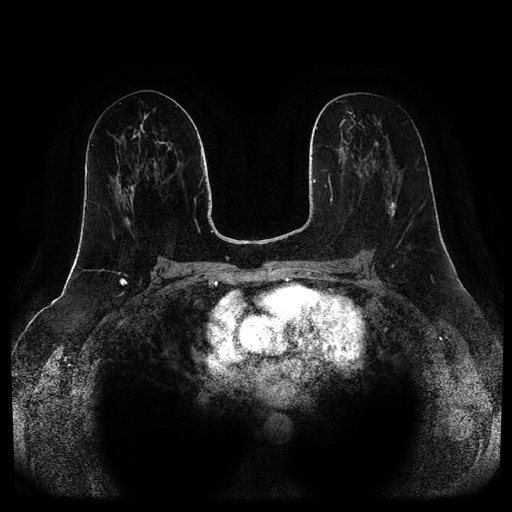
Breast MRI (dynamic contrast-enhanced, multi-phase), one axial slice; position 41 of 116 along the scan axis; dynamic contrast-enhanced series, time point 2 of 5 at this slice position (early post-contrast); 1.5 T; TE 2.6 ms, TR 5.2 ms; 2 mm slice thickness; 512 × 512 image matrix, field of view 380 × 380 mm. Female patient, age 57 years.
Outlined on this slice (semi-automatically segmented with operator editing):
- breast lesion (labelled 'tumour' in the annotation; benign lesions carry a separate 'benign' label): bounding box (x1, y1, x2, y2) in pixels: (388, 202, 396, 216)